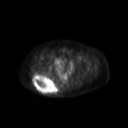
FDG PET of an extremity soft-tissue mass (from a PET/CT study), one axial slice. Slice 58 of 267 in the series (ordered by position). 3.27 mm slice thickness. 128 × 128 image matrix. Patient: female, 60 years. From the clinical record (not read from this slice): histological type: spindle cell suggestive of myxofibrosarcoma; grade: intermediate; site of the primary tumour: right buttock.
Annotated regions visible in this slice (expert contour drawn on MRI and transferred to this co-registered scan by the dataset authors):
- gross tumour volume (mass): bounding box [x1, y1, x2, y2] px = [33, 74, 58, 95]